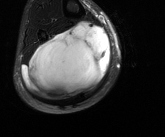
MRI of an extremity soft-tissue mass, one axial slice; position 63 of 81 along the scan axis; T2-weighted fat-saturated; MR volume resampled by the dataset authors to the PET/CT grid (not the native acquisition matrix); 3.27 mm slice thickness; 165 × 137 image matrix. Male patient. Case-level facts recorded for this patient, not image findings: histological type: liposarcoma - round cell; grade: high; site of the primary tumour: right calf.
Annotated regions visible in this slice (expert contour drawn on MRI and transferred to this co-registered scan by the dataset authors):
- gross tumour volume (mass): bounding box <21,21,111,101> (left, top, right, bottom; pixels)